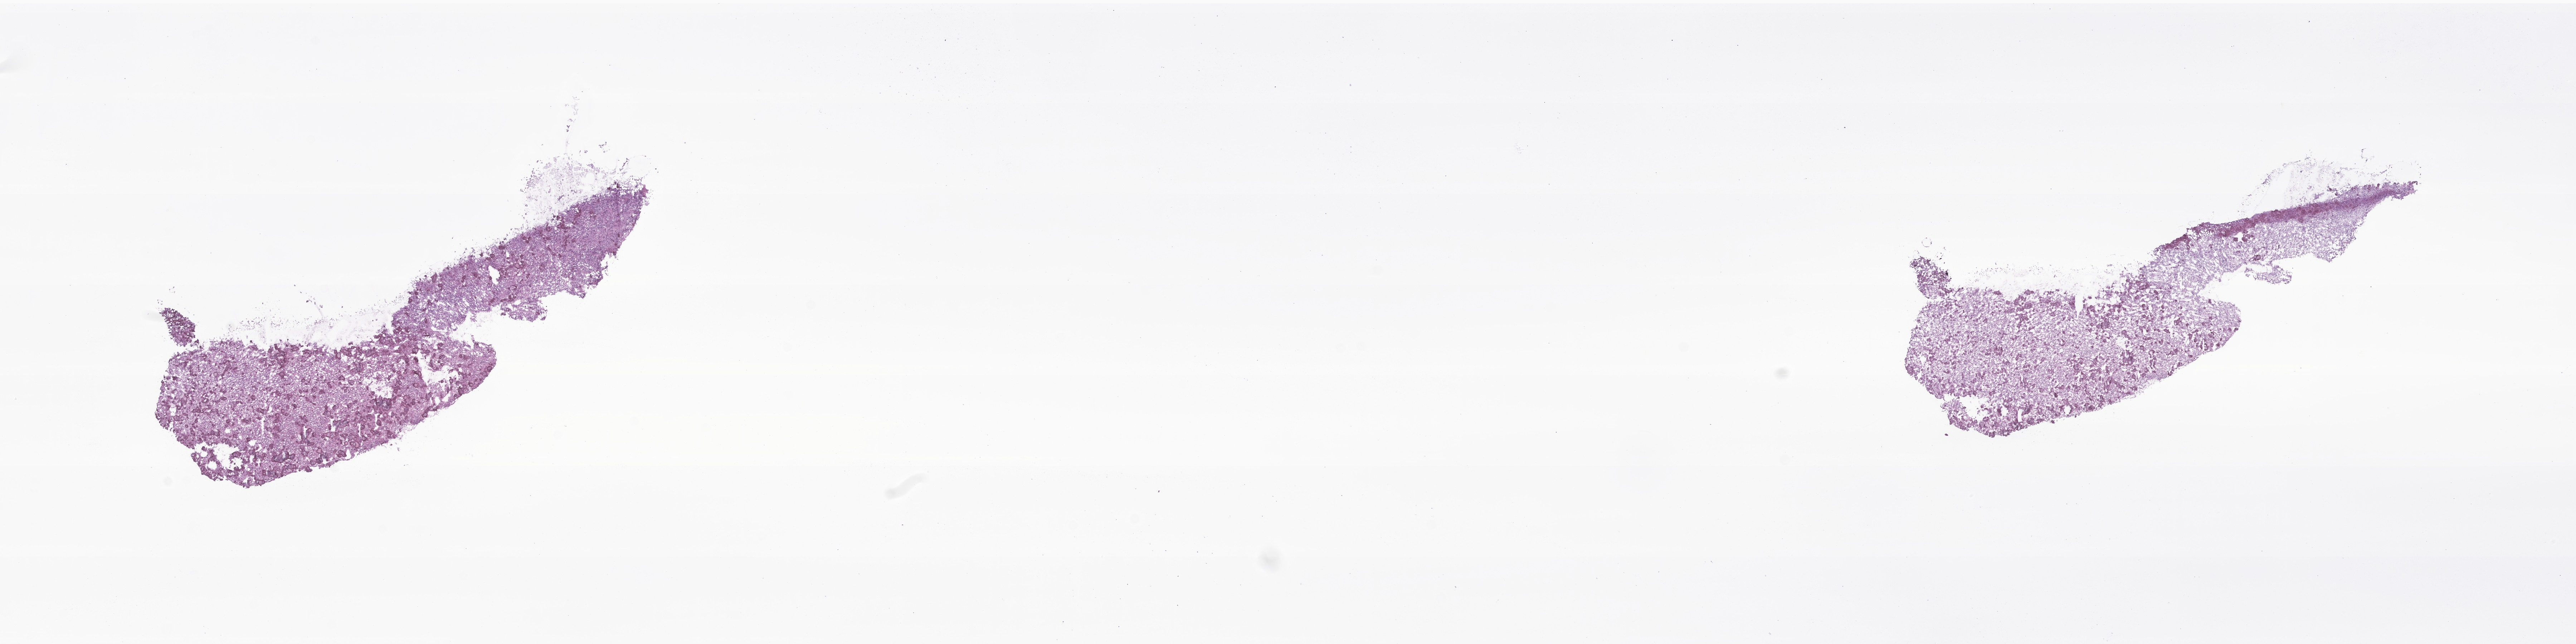
Whole-slide image, hematoxylin and eosin (H&E) stain of tumor tissue from the brain, whole scanned area (about 30.3 x 7.6 mm) shown as a low-resolution overview. Frozen section (OCT-embedded). Patient: male, age 86 months (7 years 2 months).
Diagnosis (ICD-O-3 morphology term): Ependymoma, NOS.